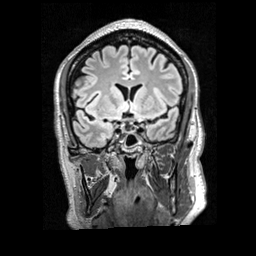
Brain MRI from a brain-tumour surgery series, one coronal slice. Slice 124 of 200 in the series (ordered by position). T2 FLAIR. 1 mm slice thickness. 256 × 256 image matrix. Case-level facts recorded for this patient, not image findings: histopathology: Glioblastoma; WHO grade: 4; IDH mutation: no.
Structures marked on this image (outlined manually by an expert reader):
- tumour: box from (x=89, y=76) to (x=93, y=78) px